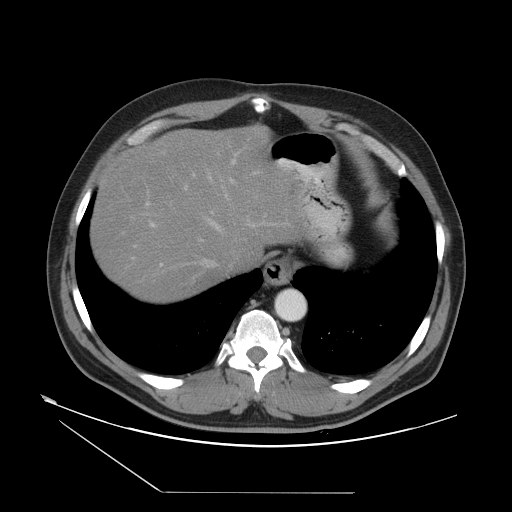
Contrast-enhanced abdominal CT, one axial slice; reconstruction kernel STANDARD; 120 kVp; intravenous contrast given; soft-tissue window (W 400 / L 40 HU); 5 mm slice thickness; 512 × 512 image matrix, field of view 454 × 454 mm. Male patient, age 59 years. From the clinical record (not read from this slice): diagnosis: colorectal cancer liver metastases, imaged before liver resection; multiple liver metastases: yes; largest metastasis: 0.3 cm; disease in both lobes: yes.
Outlined on this slice (outlined manually by an expert reader):
- hepatic veins: bounding box <182,194,280,267> (left, top, right, bottom; pixels)
- liver: <93,129,296,301>
- planned liver remnant (the part of the liver to remain after resection): <93,153,262,300>
- portal vein (with intrahepatic branches): <132,152,257,267>
- liver metastasis: <228,154,230,160>